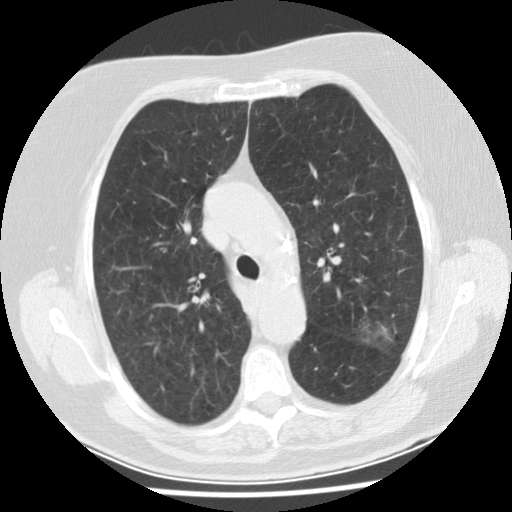
Low-dose screening chest CT, axial slice, baseline screening round, lung window (W 1500 / L -600 HU), 2.5 mm slice thickness, slice 110 of 149 in the series. Female, age 74 years at enrolment. Former smoker at enrolment.
• Lesion marked by an expert reader, bounding box (x1, y1, x2, y2) in pixels: (339, 306, 409, 361).
• The screening reader recorded 2 non-calcified nodules or masses ≥4 mm on this exam (left upper lobe, left lower lobe); which of them this box marks is not recorded.
• Official screen result: positive, change unspecified: nodule(s) >= 4 mm or enlarging nodule(s), mass(es), or other non-specific abnormalities suspicious for lung cancer.
• Participant outcome: lung cancer diagnosed 532 days after this screen (after the second annual screen) — bronchiolo-alveolar adenocarcinoma, NOS, left upper lobe, stage IA (AJCC 6th edition), 20 mm at pathology.